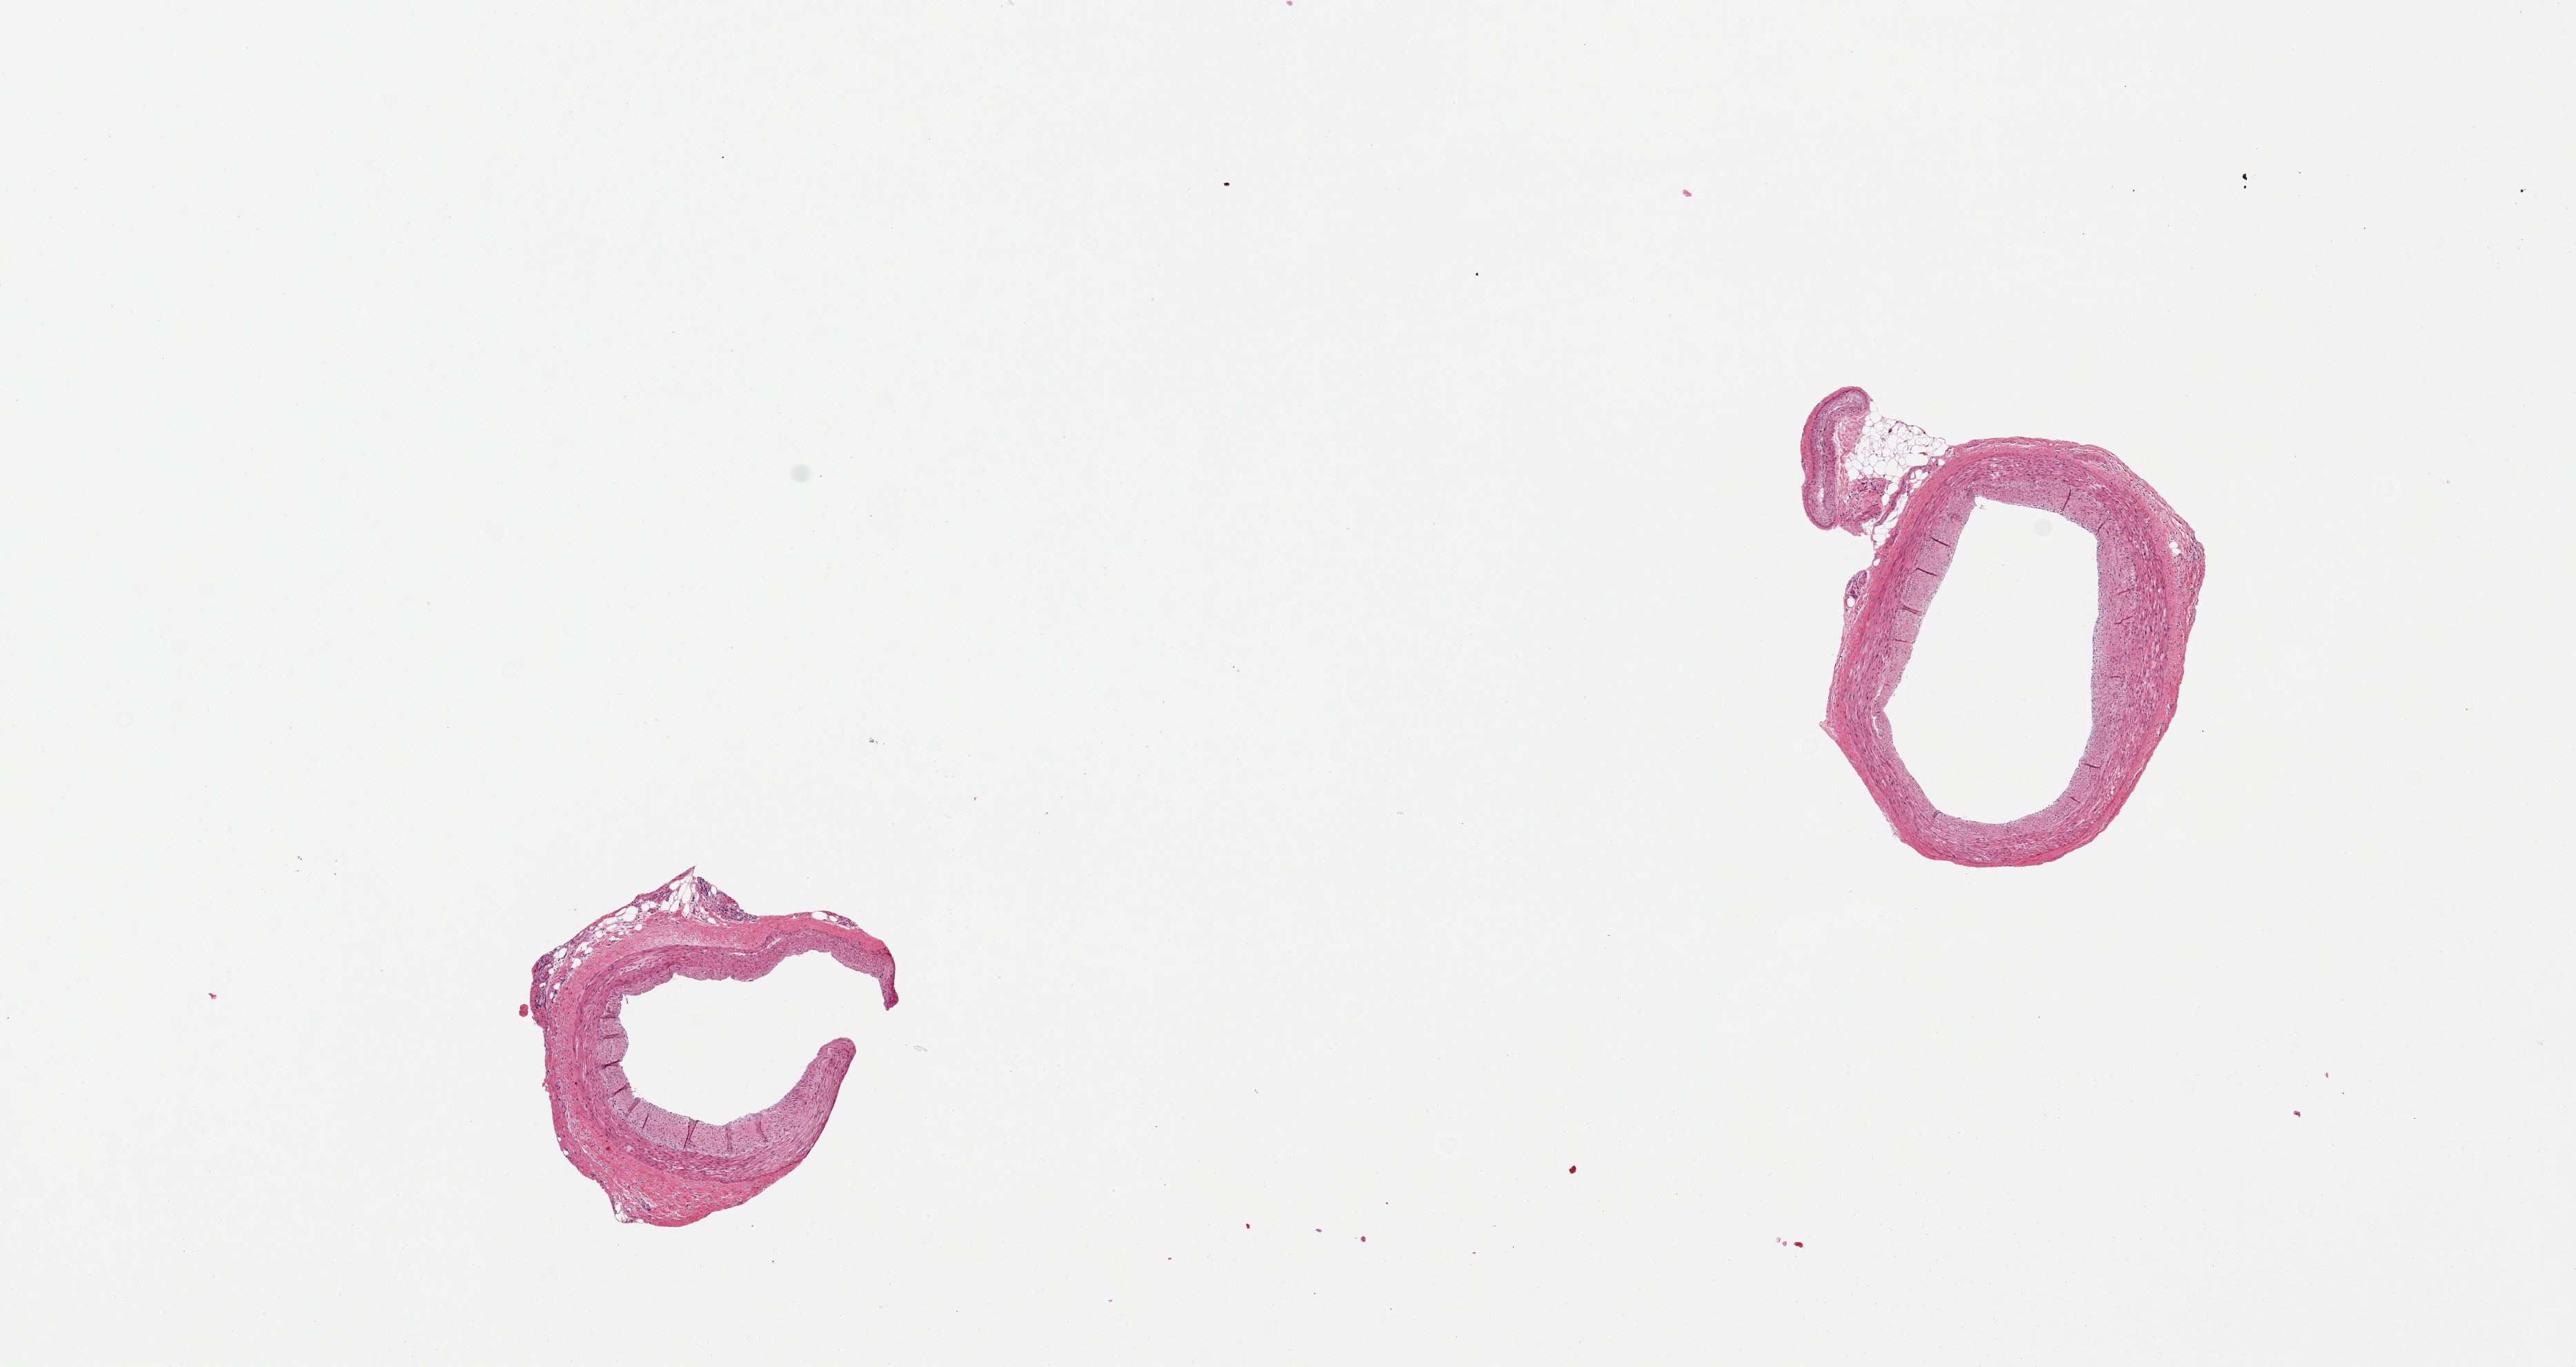
Digitized hematoxylin and eosin (H&E)-stained section — whole scanned area (about 14.8 x 7.8 mm, slide scanned at 20x) shown as a low-resolution overview, PAXgene-fixed, paraffin-embedded tissue, target tissue: coronary artery, donor tissue sample. Donor sex: male.
Reviewer comment on this tissue sample: 2 pieces, 2x2 & 3x2.5mm; no significant plaques.